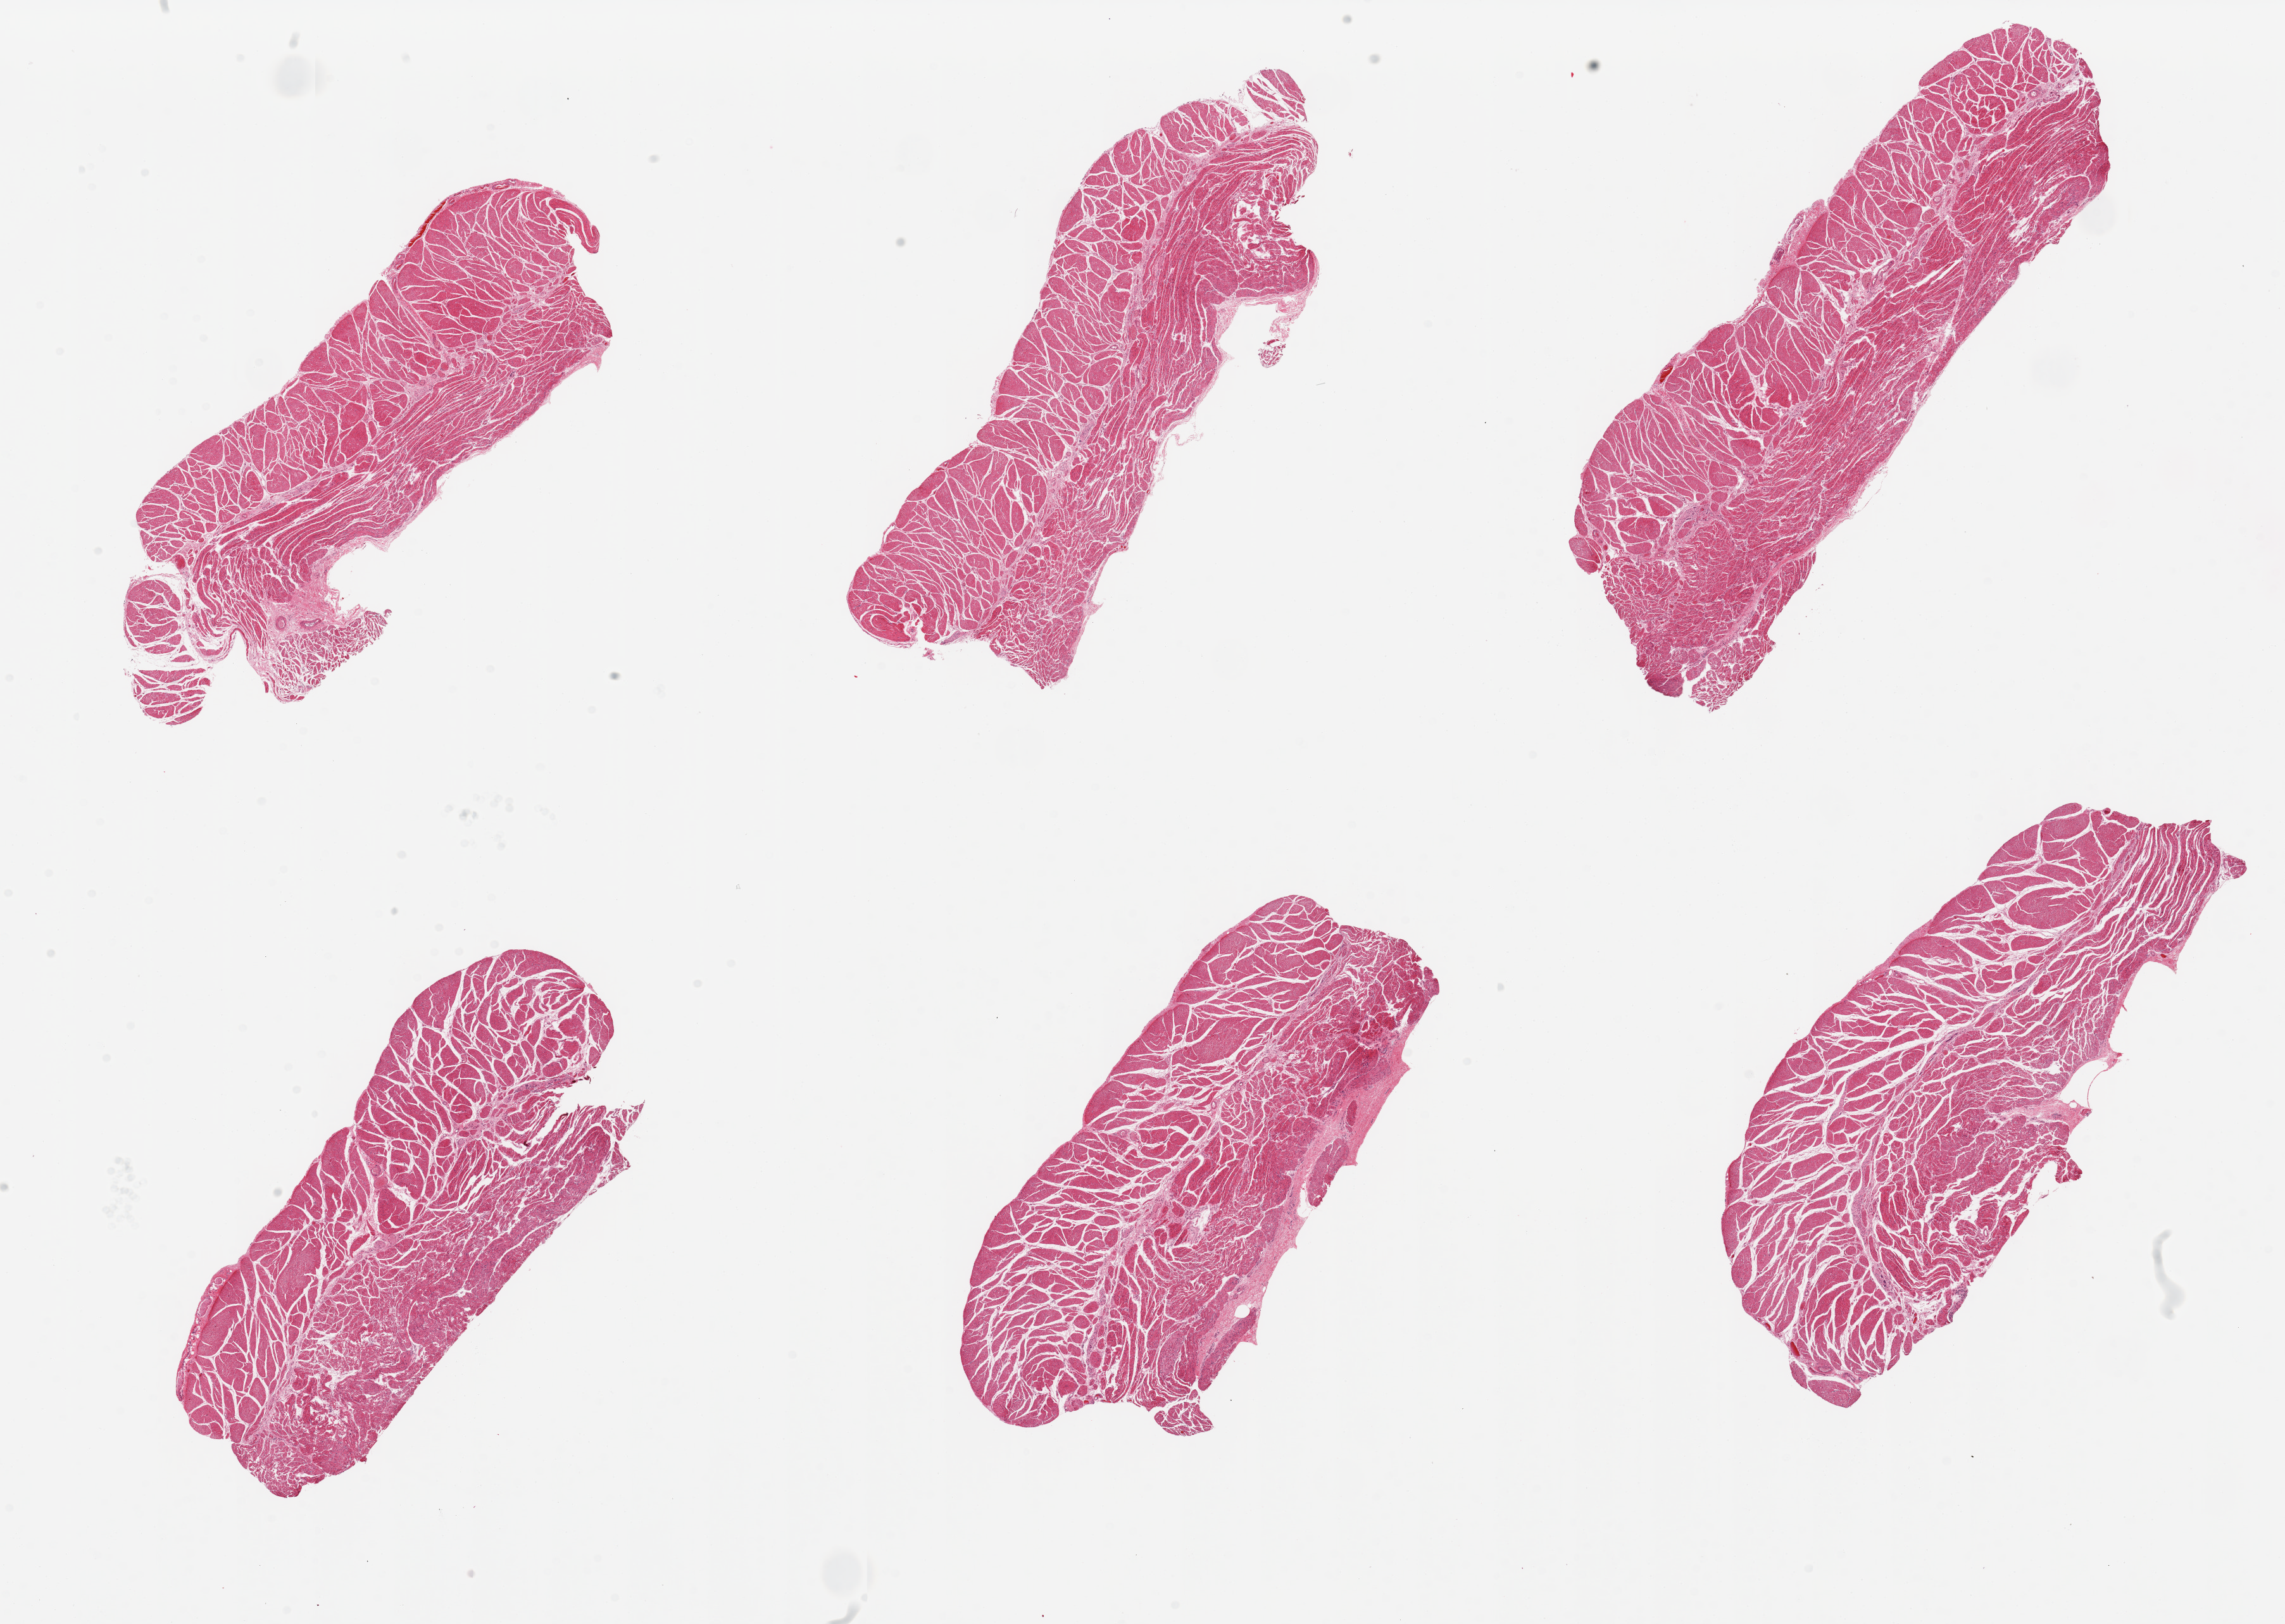
Whole-slide image, haematoxylin and eosin stain, brightfield — a low-resolution overview of the entire scanned area, about 28.5 x 20.3 mm, PAXgene-fixed, paraffin-embedded tissue, sampled site (target tissue): esophageal muscle, tissue donor sample. Male donor.
Pathologist's review note for this sample: 6 pieces, well trimmed.